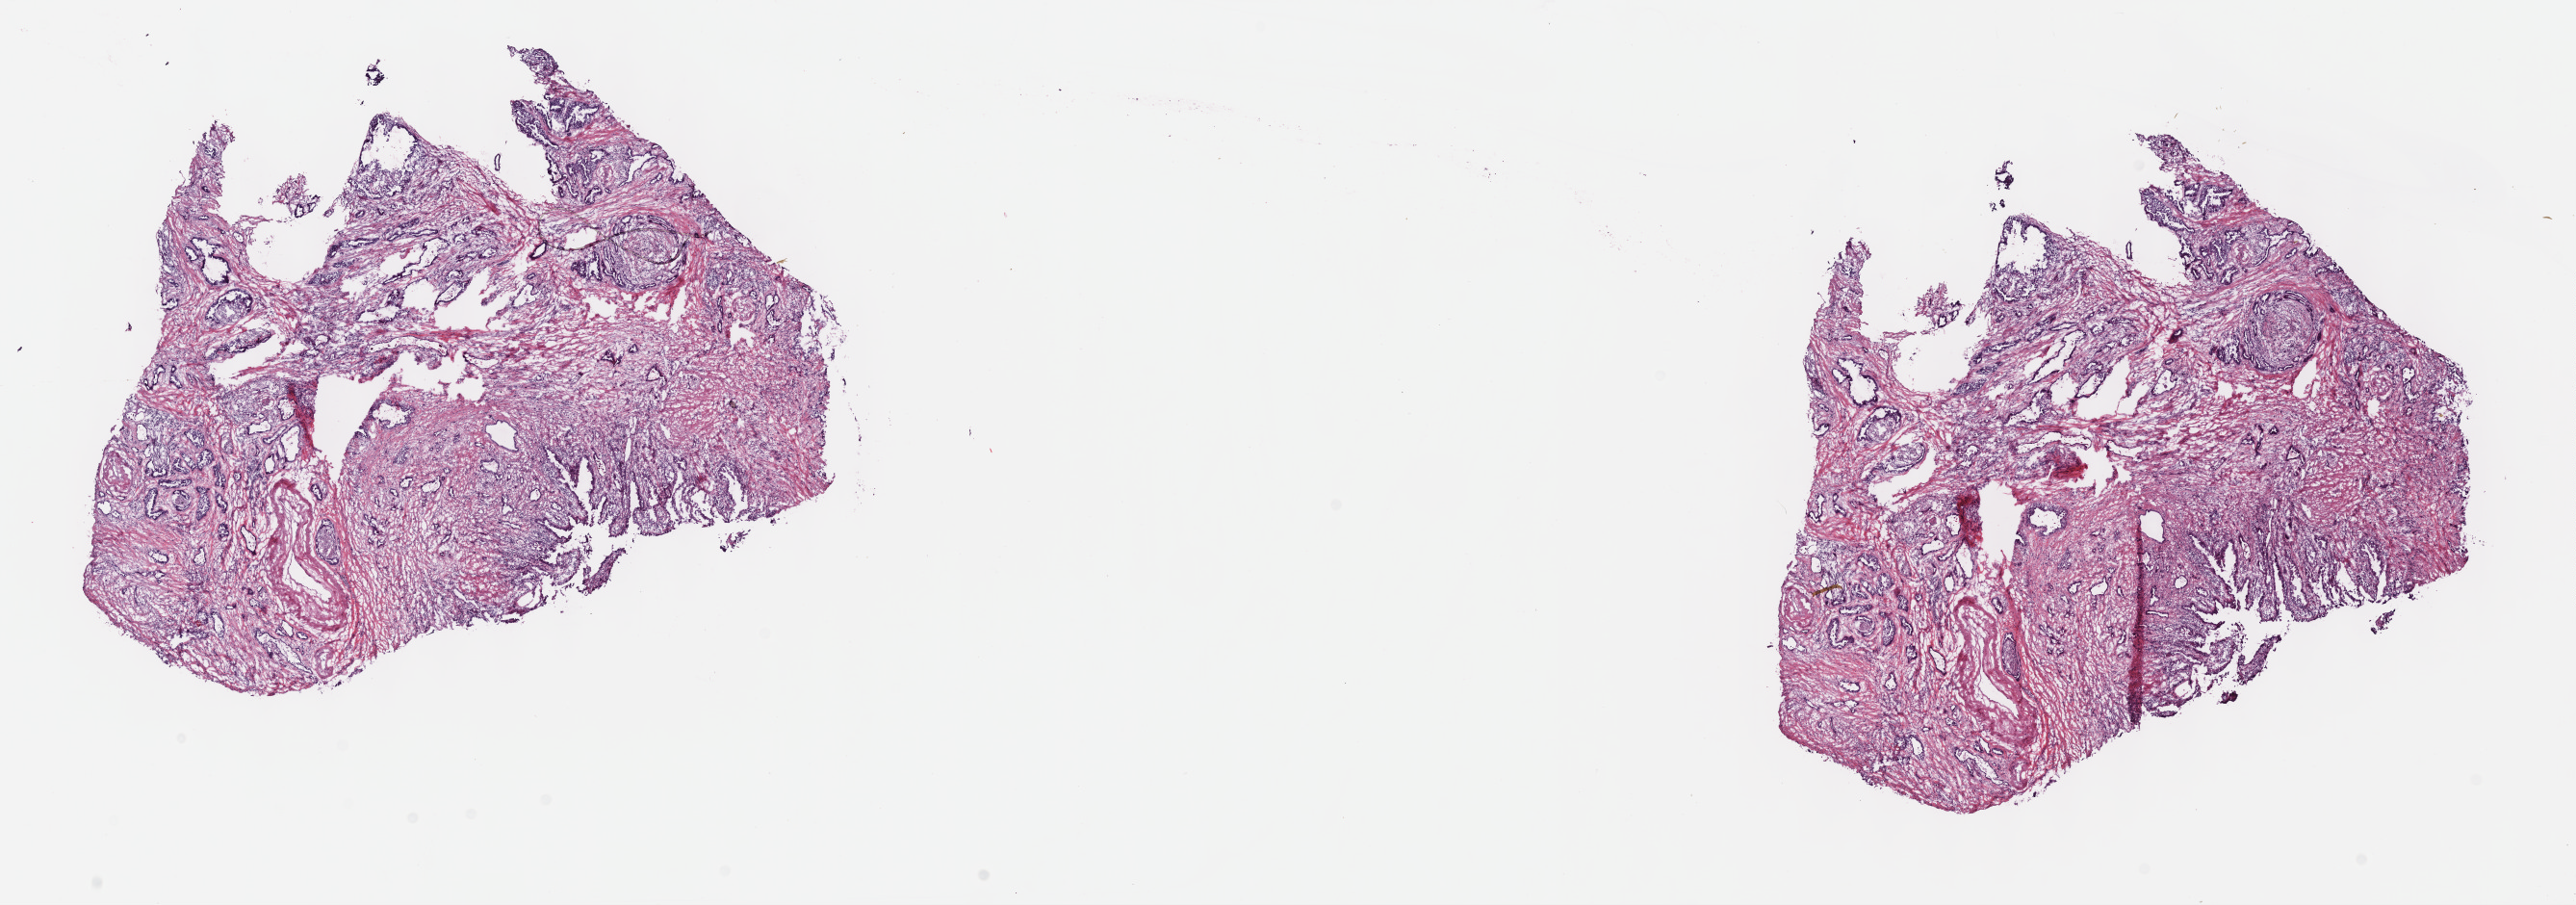
Hematoxylin and eosin (H&E) stained whole-slide image — a low-resolution overview of the entire scanned area, about 21.6 x 7.6 mm (slide scanned at 40x), frozen section from the top of the tissue portion, pancreas, primary tumour sample. Female patient; age at initial diagnosis 74 years. Histologic grade: G2 (moderately differentiated). Composition of this section per pathologist review: tumour cells 65%, tumour nuclei 65%, normal cells 10%, stromal cells 25%, necrosis 0%. Inflammatory infiltration, as recorded: lymphocyte infiltration 40%, monocyte infiltration 20%, neutrophil infiltration 20%.
AJCC pathologic stage: IIB (7th edition). Lymph nodes positive (case pathology): 7 of 26 examined. Diagnosis: Infiltrating duct carcinoma, NOS (head of pancreas).